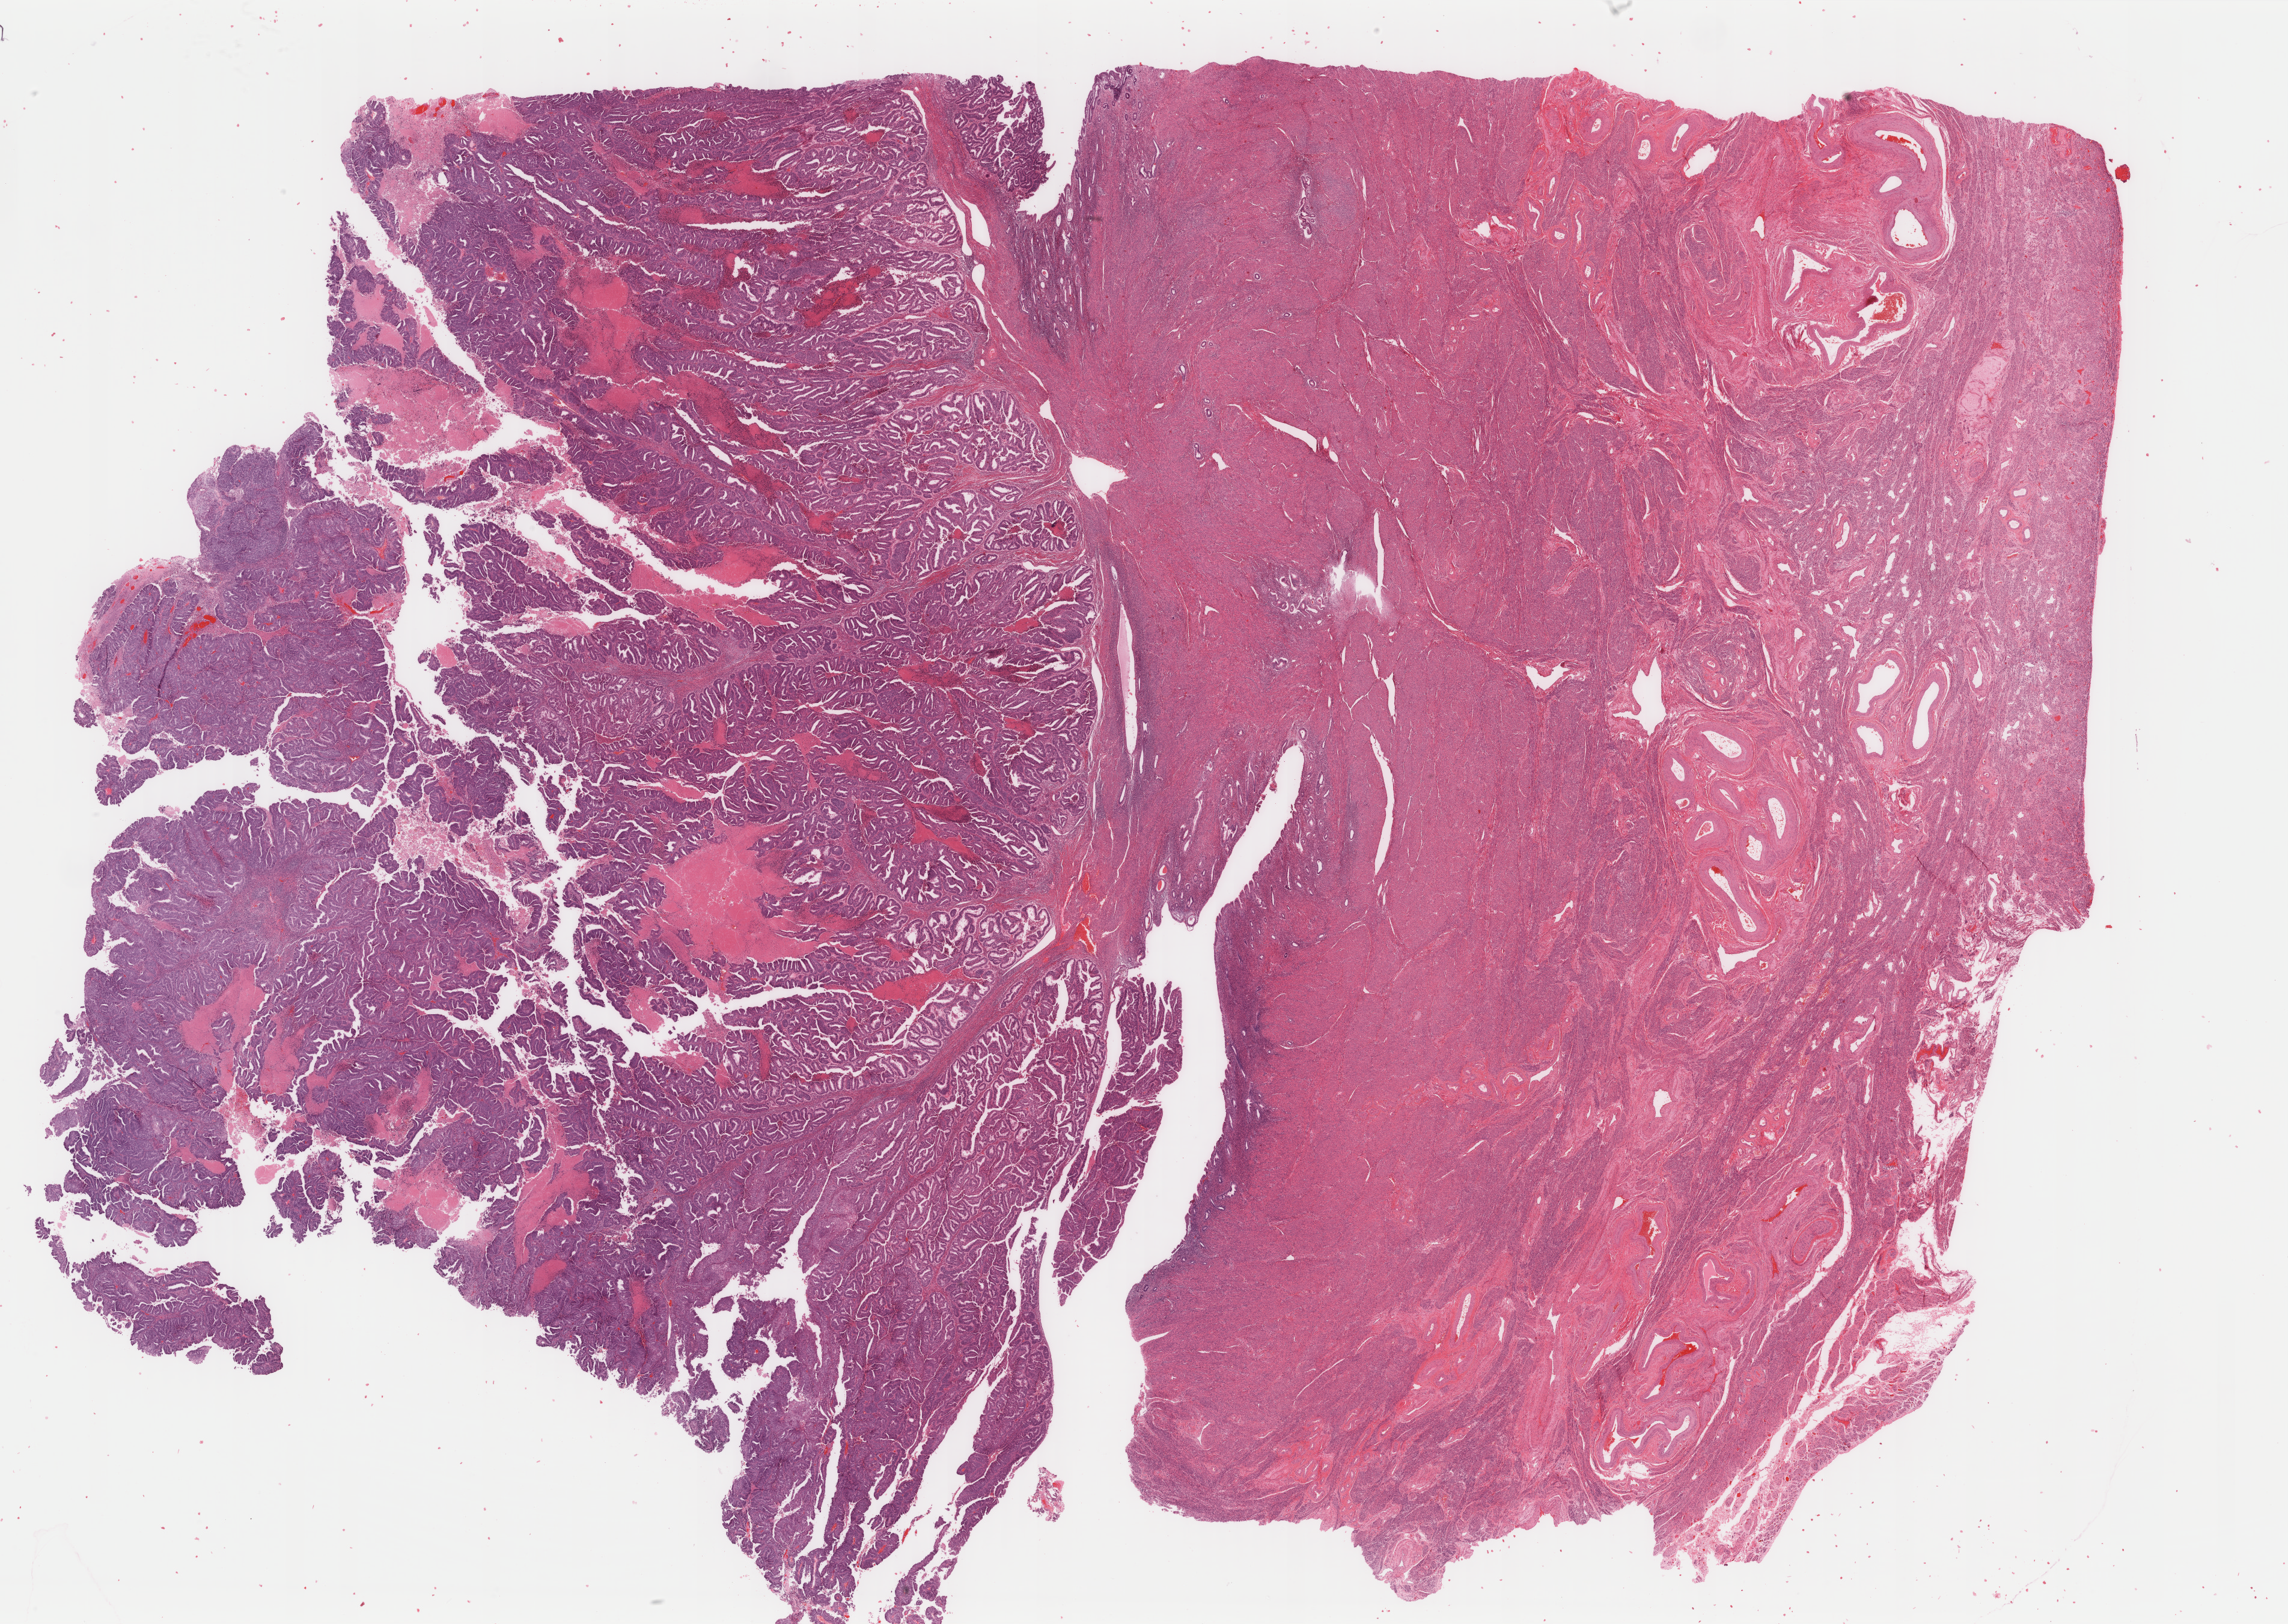
Whole-slide histology image, Hematoxylin and eosin (H&E) stained, low-resolution overview of the scanned area, about 30.2 x 21.5 mm; formalin-fixed paraffin-embedded (FFPE) diagnostic section; primary tumour sample from the uterus. Patient: female, age at initial diagnosis 47 years.
Pathologic diagnosis: Endometrioid adenocarcinoma, NOS (endometrium).